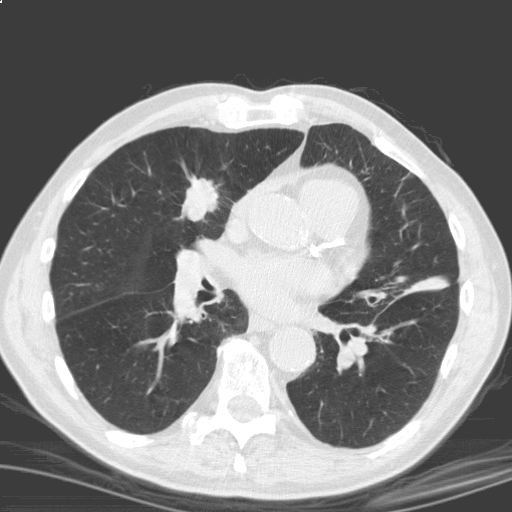
Chest CT (low-dose screening protocol), one axial image. Second screening round (one year after baseline). Lung window (W 1500 / L -600 HU). Standard (soft-tissue) reconstruction kernel (C). Slice 92 of 184 in the series. 512 × 512 image matrix, field of view 329 × 329 mm. Male, age 69 years at enrolment.
• Expert reader's lesion annotation, bounding box <169,164,232,225> (left, top, right, bottom; pixels).
• The screening reader recorded 2 non-calcified nodules or masses ≥4 mm on this exam (right upper lobe, left lower lobe); which of them this box marks is not recorded.
• Later outcome: lung cancer diagnosed 17 days after this screen — squamous cell carcinoma, NOS, right upper lobe, moderately differentiated (G2), stage IB (AJCC 6th edition), 40 mm at pathology.